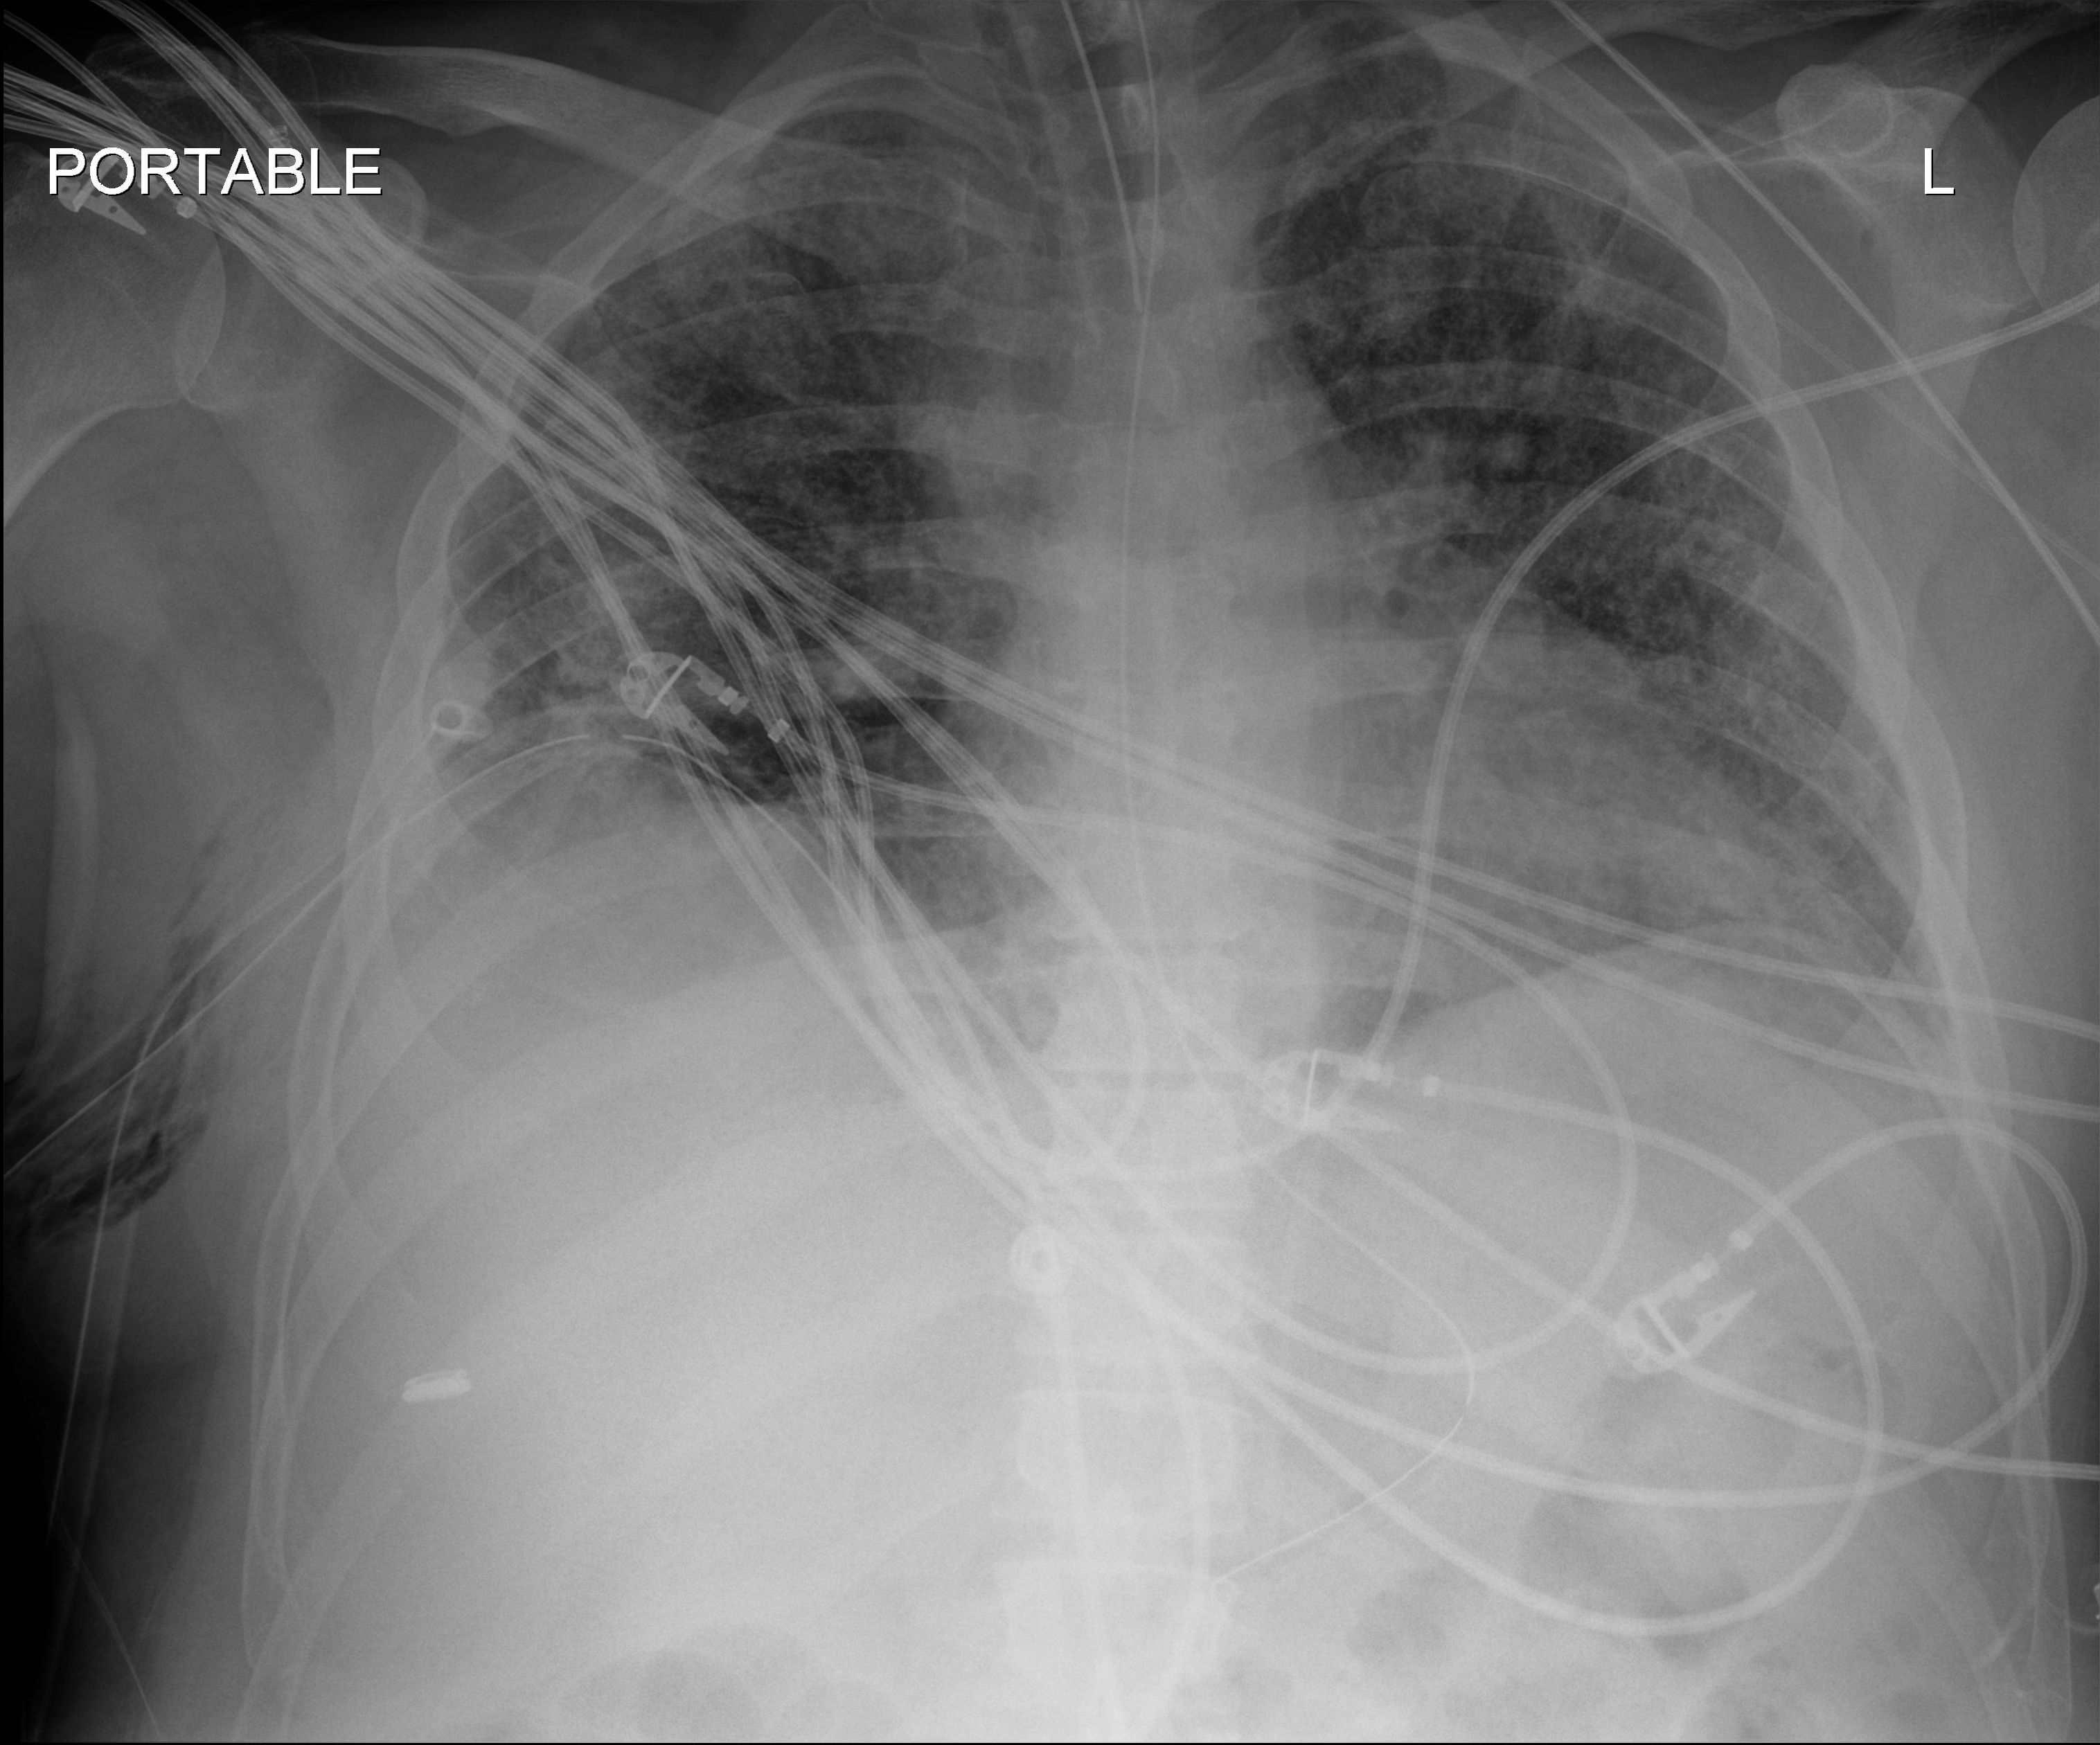
Portable chest radiograph, anteroposterior (AP) projection. Male patient hospitalised with COVID-19, age 18–59 years.
Admission-level facts for this patient (not findings on this image; timing relative to this image not recorded): mechanically ventilated during this hospital stay: yes; diabetes (admission record): no.